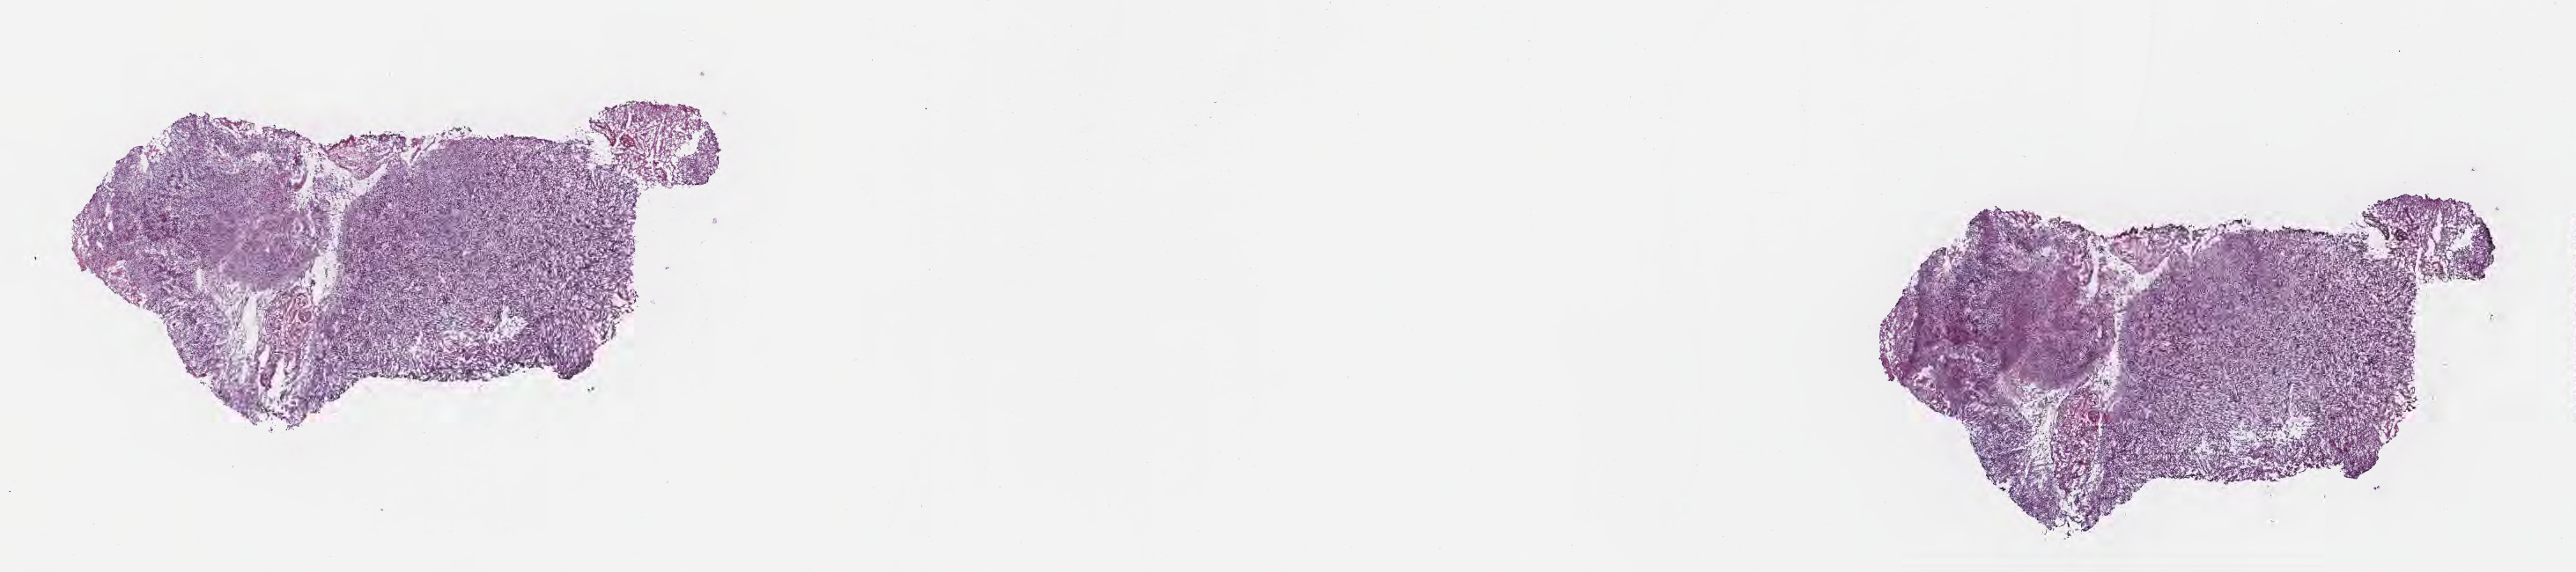
Whole-slide image, haematoxylin and eosin stain — a low-resolution overview of the entire scanned area, about 23.6 x 5.3 mm; frozen section; primary tumor; anatomic site: brain. Male, age 37 years at initial diagnosis. Pathologist review of this section (percent, as recorded): tumor cells 59%, tumor nuclei 71%.
Histologic diagnosis: Glioblastoma, NOS.